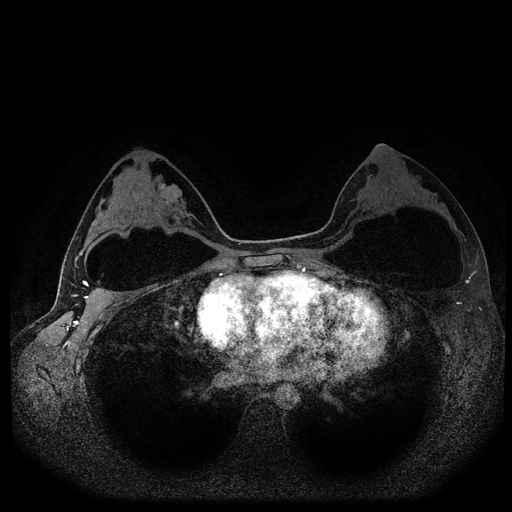
Breast MRI (dynamic contrast-enhanced, multi-phase), one axial slice; slice 62 of 116 in the series (ordered by position); dynamic contrast-enhanced series, time point 2 of 5 at this slice position (early post-contrast); 1.5 T; TE 2.6 ms, TR 5.4 ms; 2 mm slice thickness; 512 × 512 image matrix, field of view 340 × 340 mm. Patient: female, 33 years.
Outlined on this slice (semi-automatic segmentation, software-assisted and operator-edited):
- breast lesion (labelled benign in the annotation): bounding box <158,180,183,205> (left, top, right, bottom; pixels)